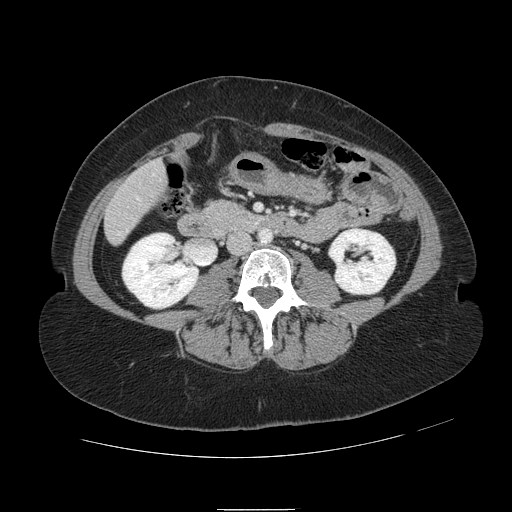
Contrast-enhanced abdominal CT, one axial slice; position 14 of 121 along the scan axis; 120 kVp; intravenous contrast given; soft-tissue window (W 400 / L 40 HU); 2.5 mm slice thickness; 512 × 512 image matrix, field of view 400 × 400 mm. Female patient, age 52 years. Case-level facts recorded for this patient, not image findings: diagnosis: colorectal cancer liver metastases, imaged before liver resection; multiple liver metastases: yes; largest metastasis: 6.3 cm.
Outlined on this slice (outlined manually by an expert reader):
- hepatic veins: box from (x=119, y=174) to (x=154, y=235) px
- liver: (x=106, y=163)–(x=166, y=242)